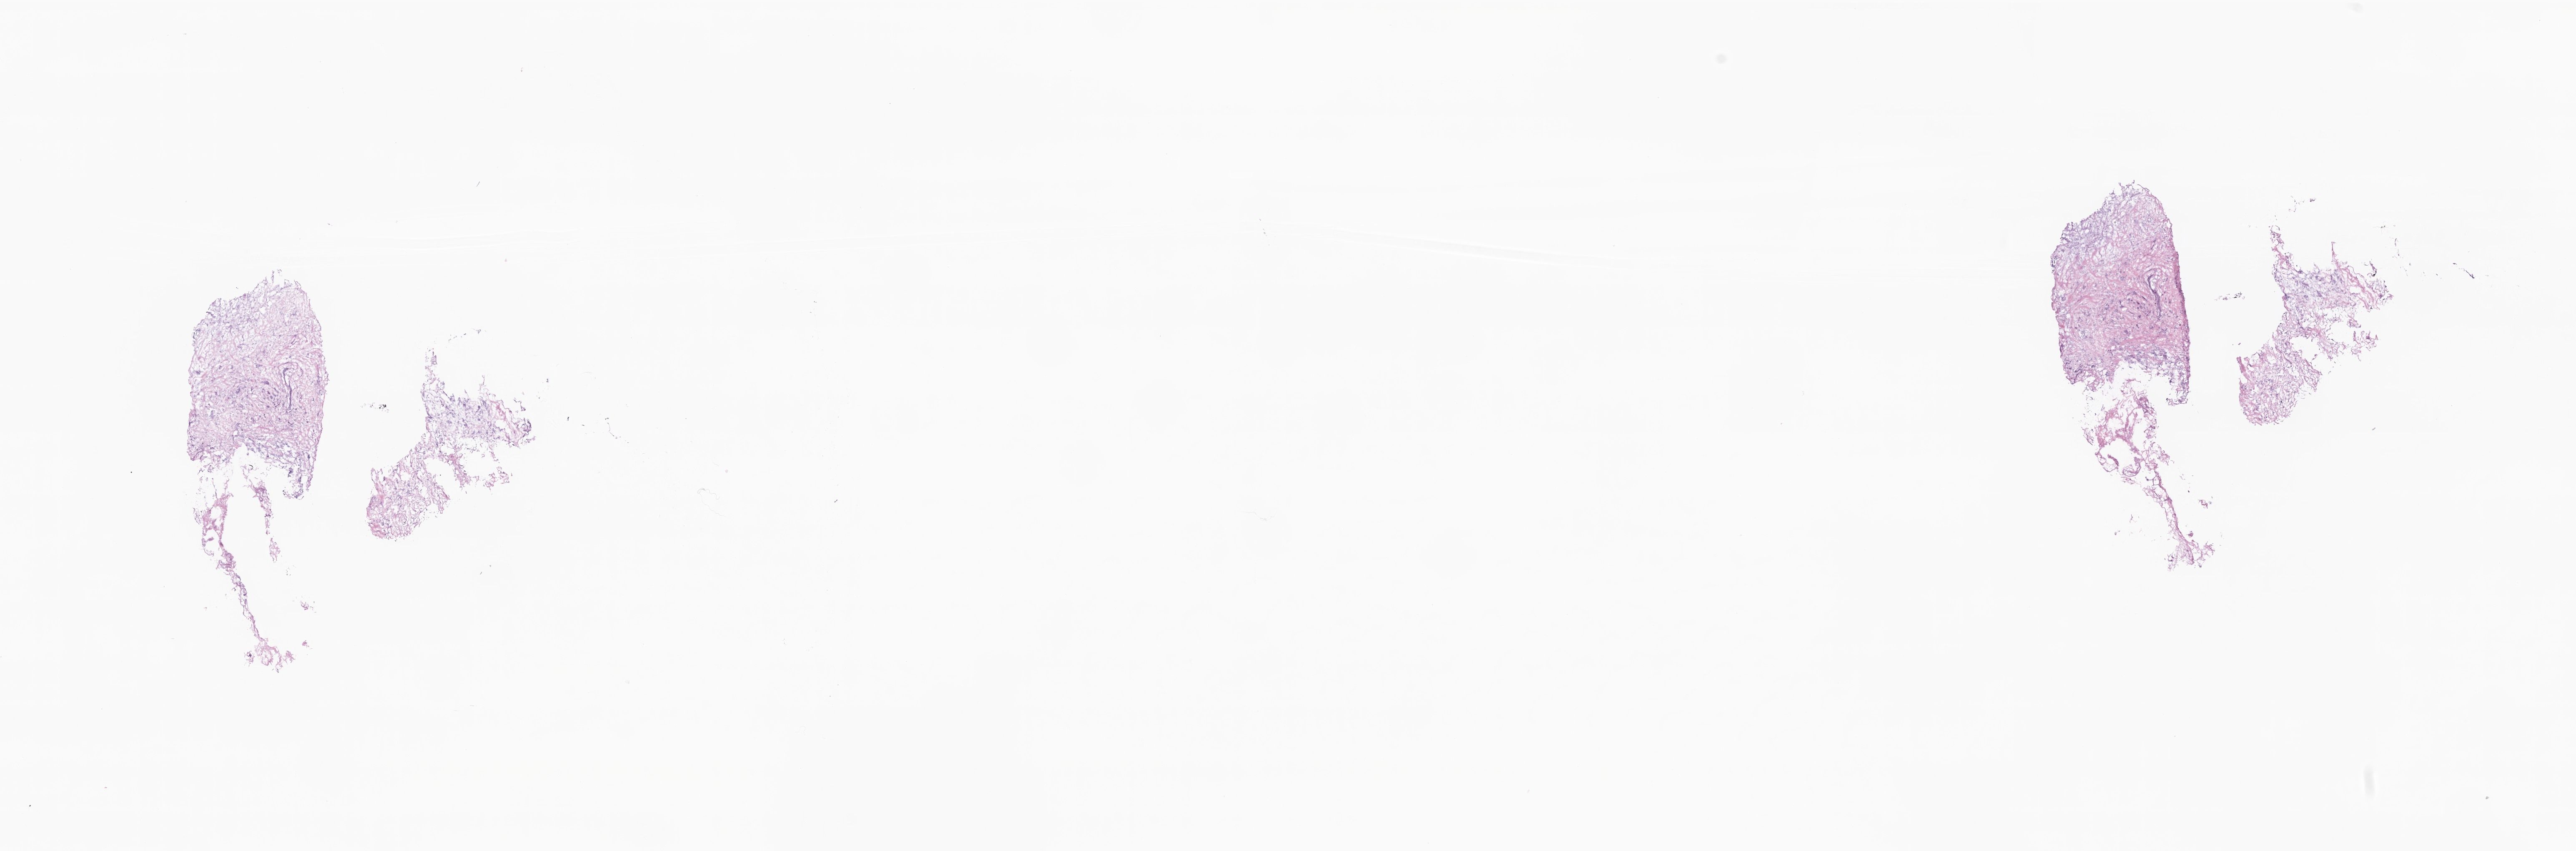
Whole-slide image, H&E stain — whole scanned area (about 26.1 x 8.6 mm) shown as a low-resolution overview; cryosection; primary tumor; site: breast (left). Female patient; age at initial diagnosis 82 years. Slide review estimates, as recorded: tumor cells 10%, tumor nuclei 10%.
Diagnosis: Infiltrating duct carcinoma, NOS.